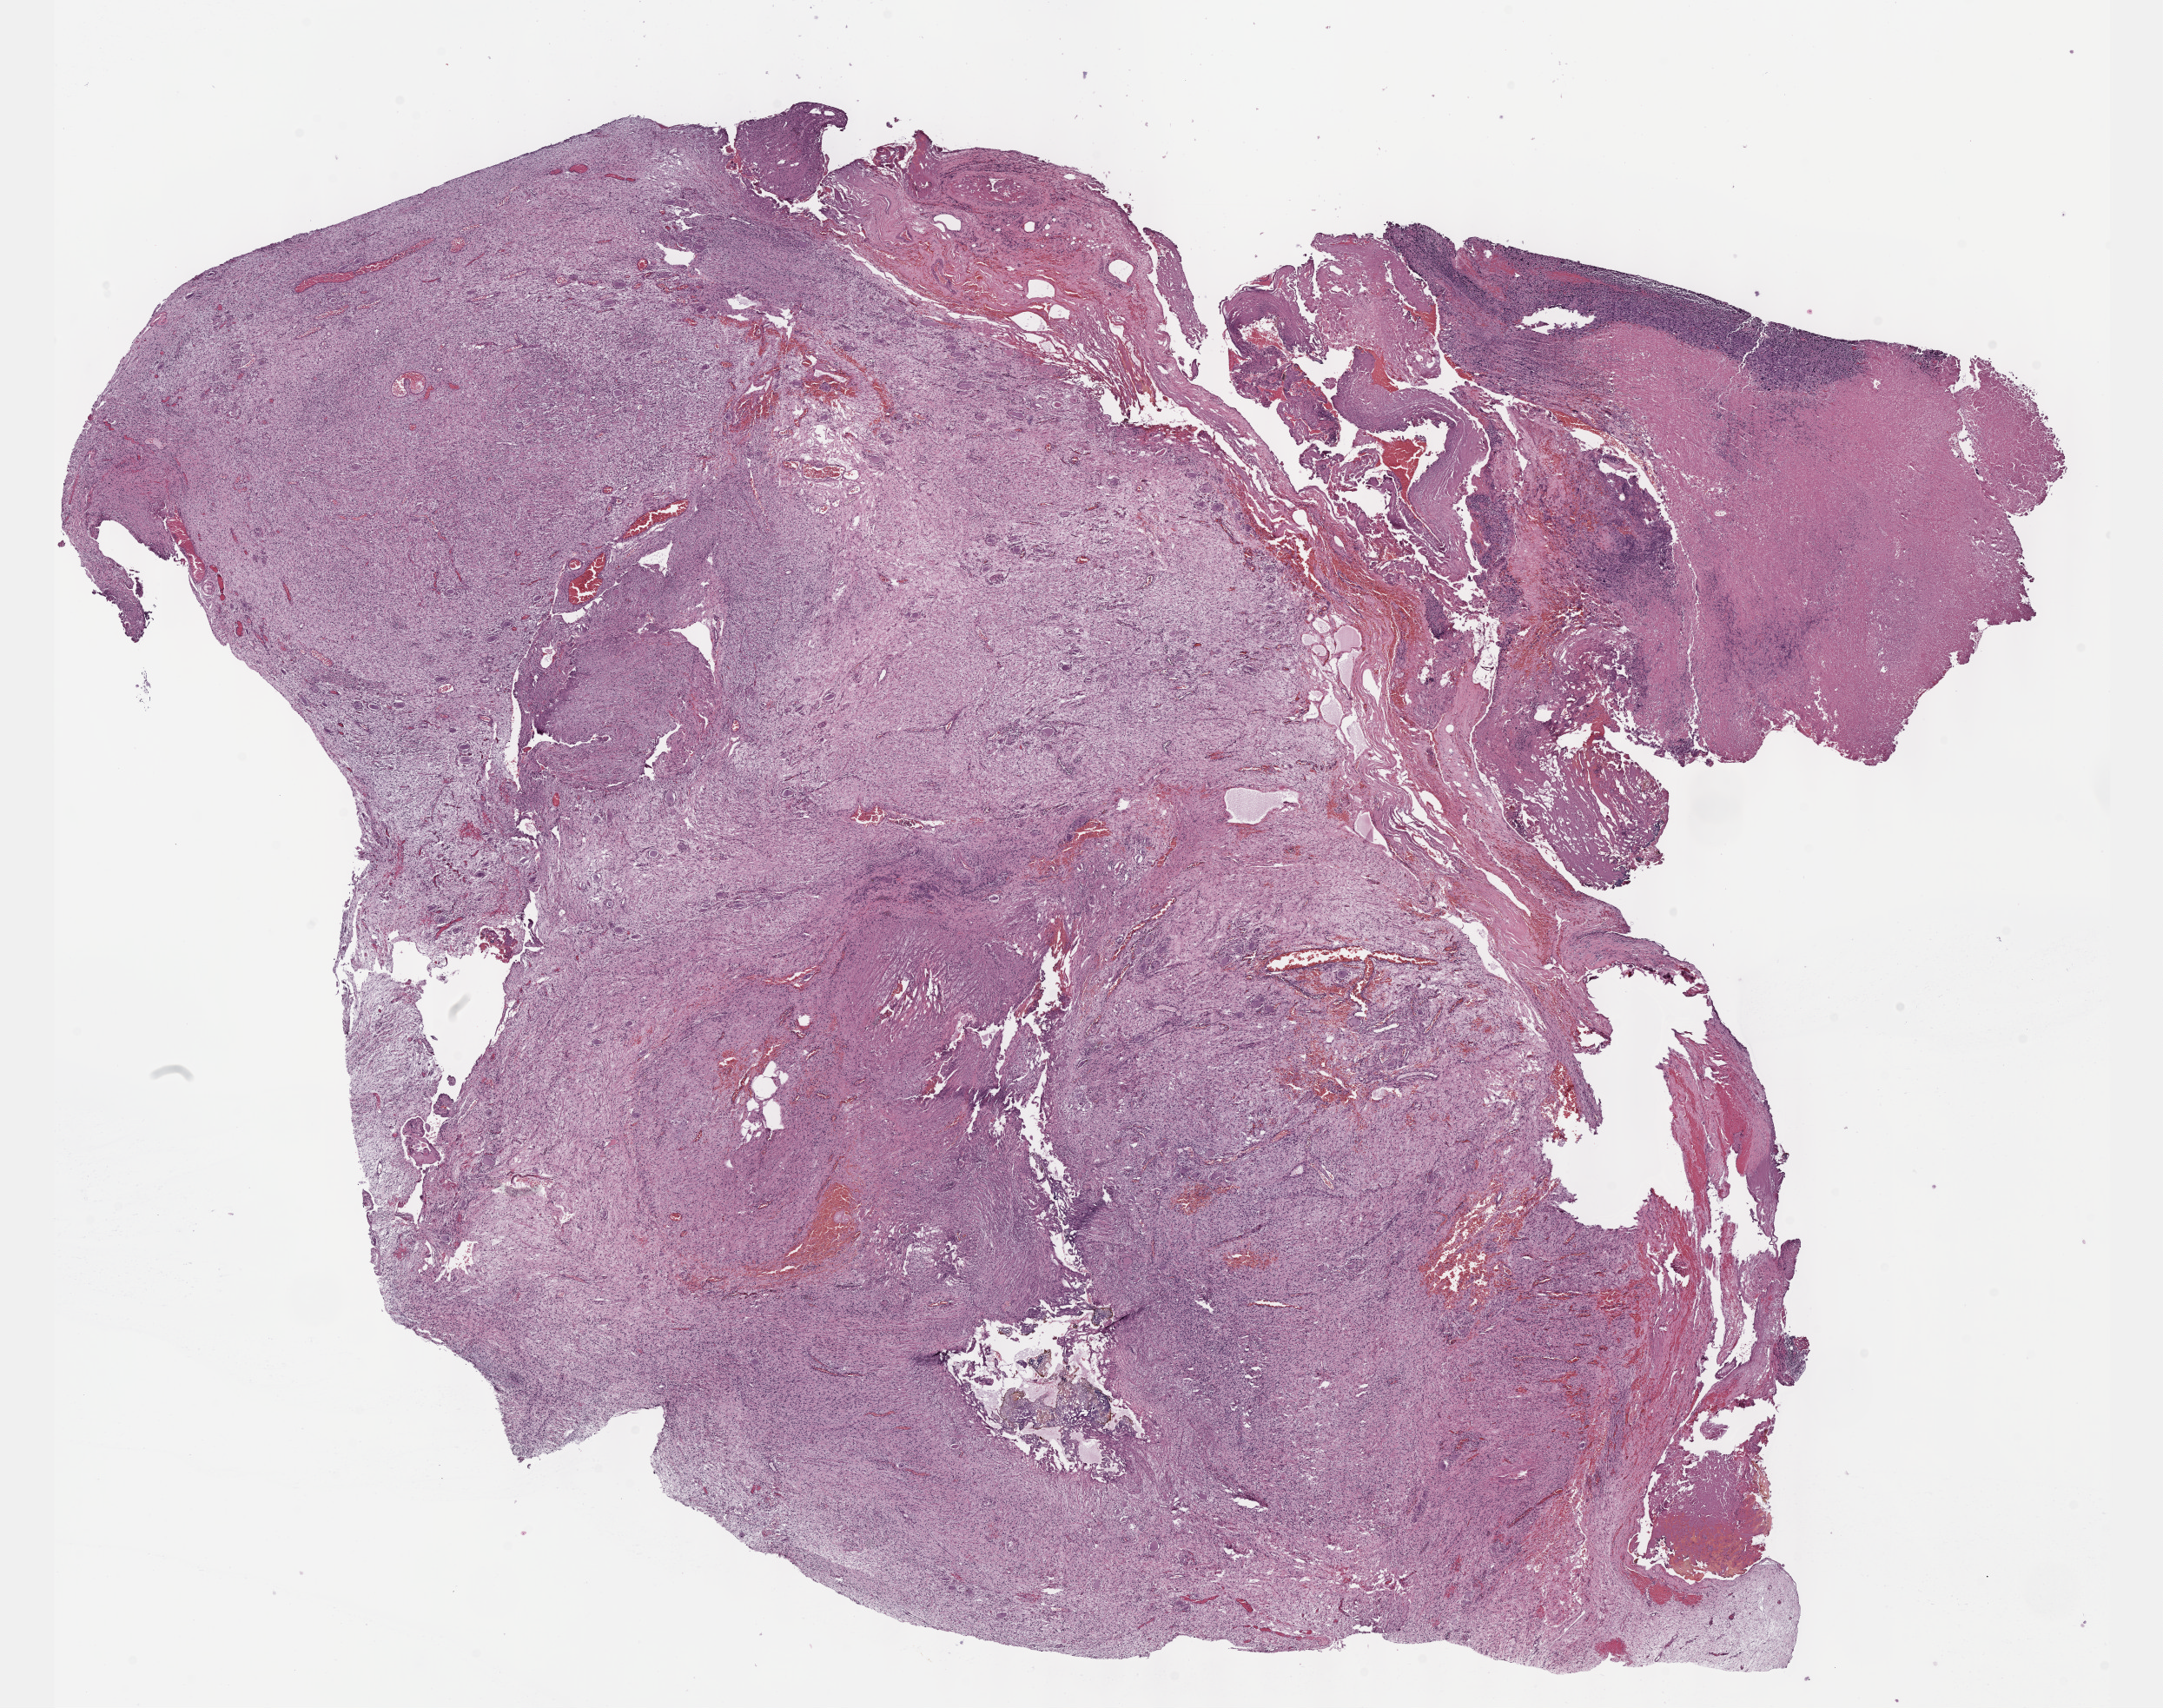
Digitized H&E tissue section (whole slide) — a low-resolution overview of the entire scanned area, about 20.1 x 15.9 mm (slide scanned at 40x), formalin-fixed paraffin-embedded (FFPE) diagnostic section, peripheral nerves and autonomic nervous system, primary tumour sample. Patient: male, age at initial diagnosis 50 years.
Pathologic diagnosis: Malignant peripheral nerve sheath tumor.